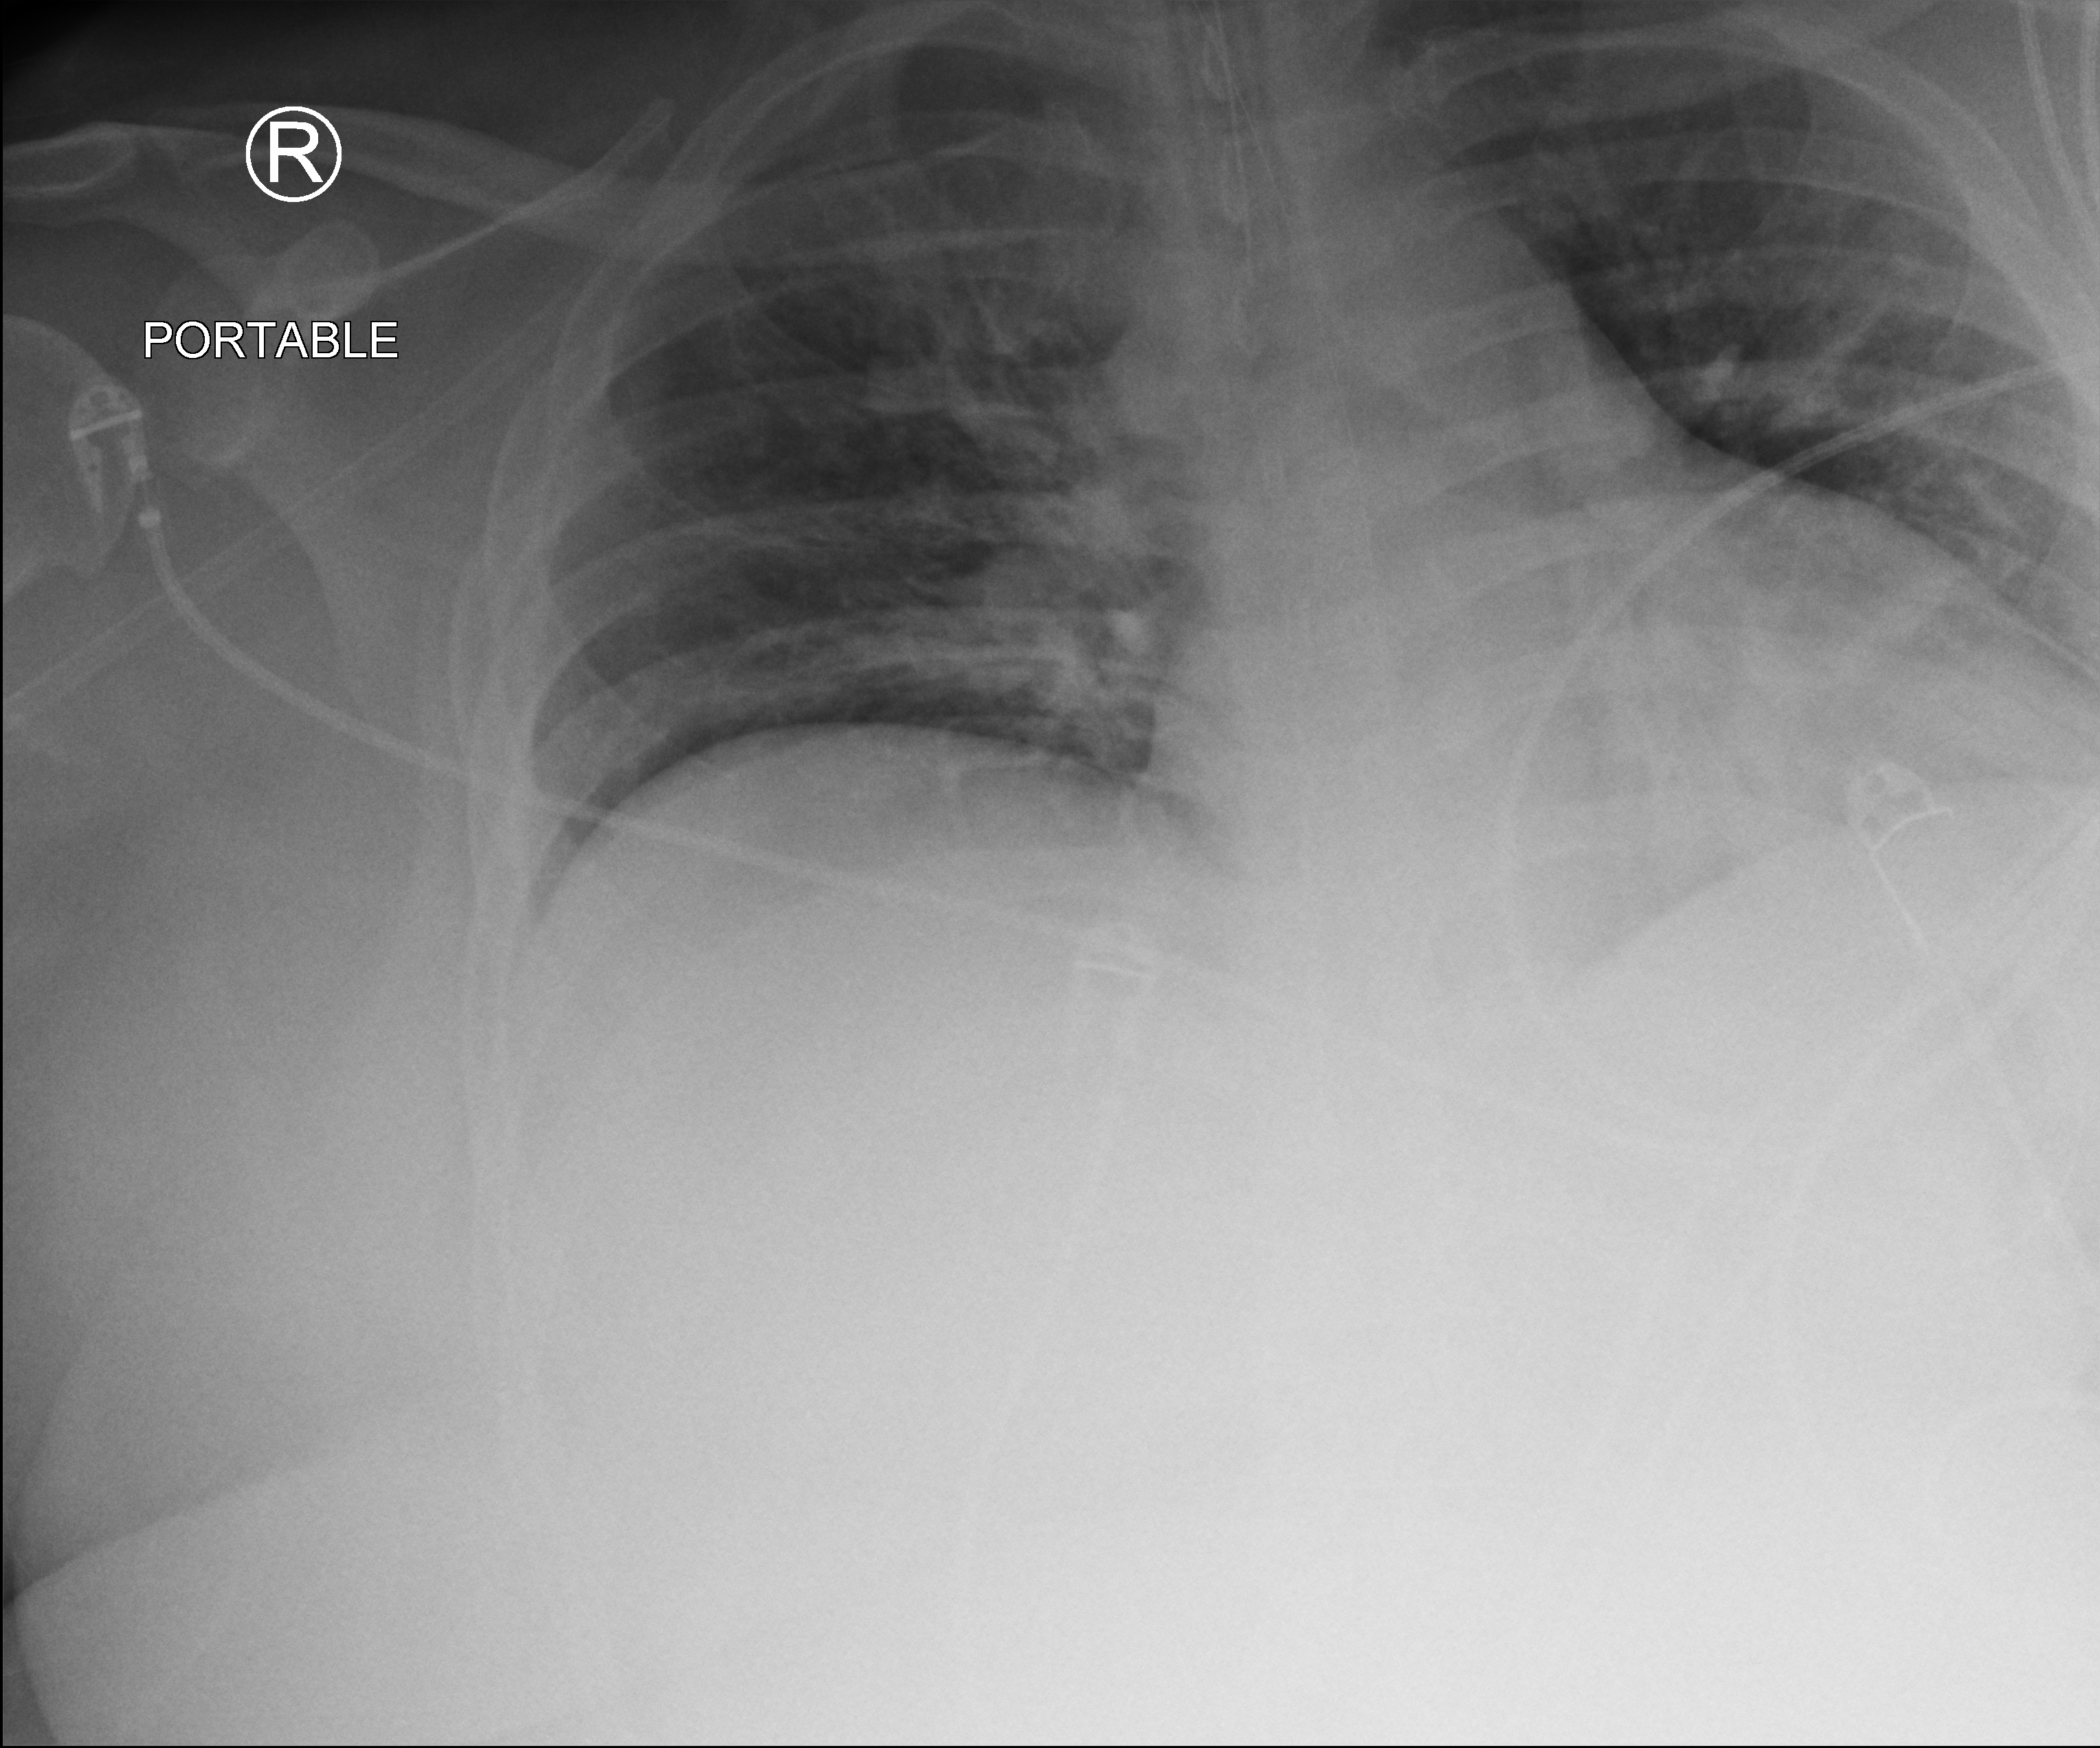
Bedside chest radiograph (computed radiography); anteroposterior (AP) projection. Male patient hospitalised with COVID-19, age 18–59 years.
Hospital-stay facts (about this admission, not read from this image; timing relative to this image not recorded): hypertension (admission record): no.